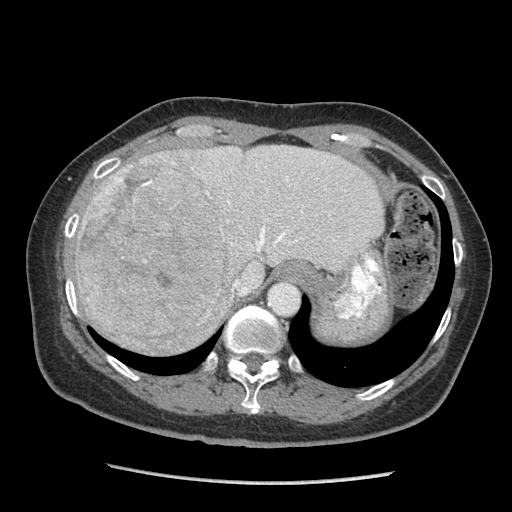
Contrast-enhanced abdominal CT (liver protocol), one axial slice; slice 70 of 105 in the series (ordered by position); reconstruction kernel STANDARD; soft-tissue window (W 400 / L 40 HU); 2.5 mm slice thickness; 512 × 512 image matrix, field of view 340 × 340 mm. From the clinical record (not read from this slice): diagnosis: hepatocellular carcinoma (patient treated with transarterial chemoembolisation; whether this scan precedes or follows treatment is not stated here); TNM stage (as recorded): Stage-I; Child-Pugh class: A; tumour differentiation: moderately differentiated; tumour nodularity: uninodular.
Annotated regions visible in this slice (semi-automatic segmentation, software-assisted and operator-edited):
- abdominal aorta: box from (x=268, y=282) to (x=299, y=315) px
- liver parenchyma outside the tumour (the mass and vessels are separate outlines, so this box may not span the whole liver): (x=74, y=144)–(x=384, y=352)
- mass: (x=74, y=154)–(x=230, y=354)
- liver vessels: (x=227, y=178)–(x=335, y=252)